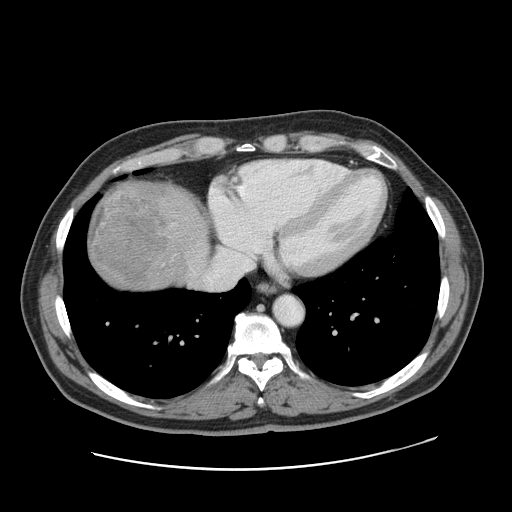
Contrast-enhanced abdominal CT, one axial slice; position 152 of 178 along the scan axis; 120 kVp; intravenous contrast given; soft-tissue window (W 400 / L 40 HU); 2.5 mm slice thickness; 512 × 512 image matrix. Male patient, age 63 years. From the clinical record (not read from this slice): diagnosis: colorectal cancer liver metastases, imaged before liver resection; multiple liver metastases: yes; largest metastasis: 8 cm; chemotherapy before resection: no.
Outlined on this slice (outlined manually by an expert reader):
- liver: bounding box <86,181,209,293> (left, top, right, bottom; pixels)
- planned liver remnant (the part of the liver to remain after resection): <189,198,196,210>
- liver metastasis: <90,184,164,284>